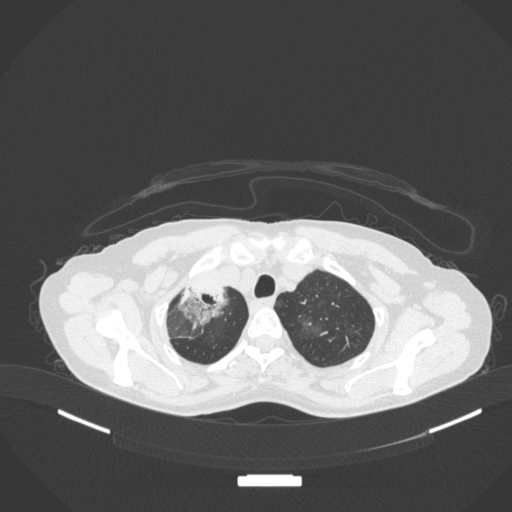
Chest CT, one axial slice; slice 280 of 311 in the series (ordered by position); lung window (W 1500 / L -600 HU); 1 mm slice thickness; 512 × 512 image matrix. Patient: female, 59 years. From the clinical record (not read from this slice): clinical TNM (as recorded): T3 N0 M0; histopathological grade: G1.
Structures marked on this image (bounding box drawn by a radiologist):
- lung tumour (recorded histology: adenocarcinoma): bounding box <173,281,228,330> (left, top, right, bottom; pixels)